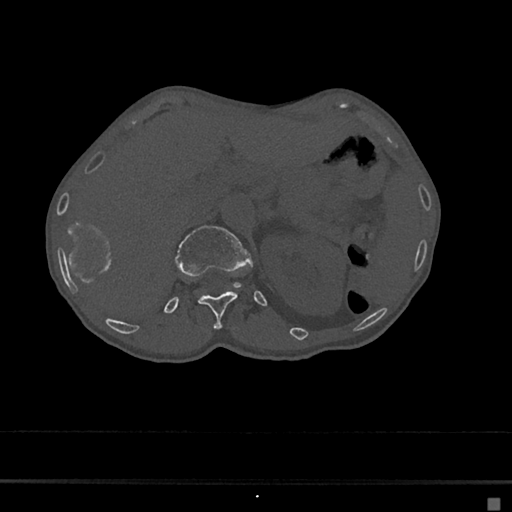
CT including the spine, one axial slice; position 106 of 797 along the scan axis; reconstruction kernel Br40s/3; 120 kVp; bone window (W 1800 / L 400 HU); 0.5 mm slice thickness; 512 × 512 image matrix. Female patient, age 68 years. From the clinical record (not read from this slice): primary cancer: renal.
Outlined on this slice (semi-automatic segmentation, software-assisted and operator-edited):
- L1 vertebra: bounding box (x1, y1, x2, y2) in pixels: (174, 225, 250, 286)
- T12 vertebra: (198, 291, 237, 328)